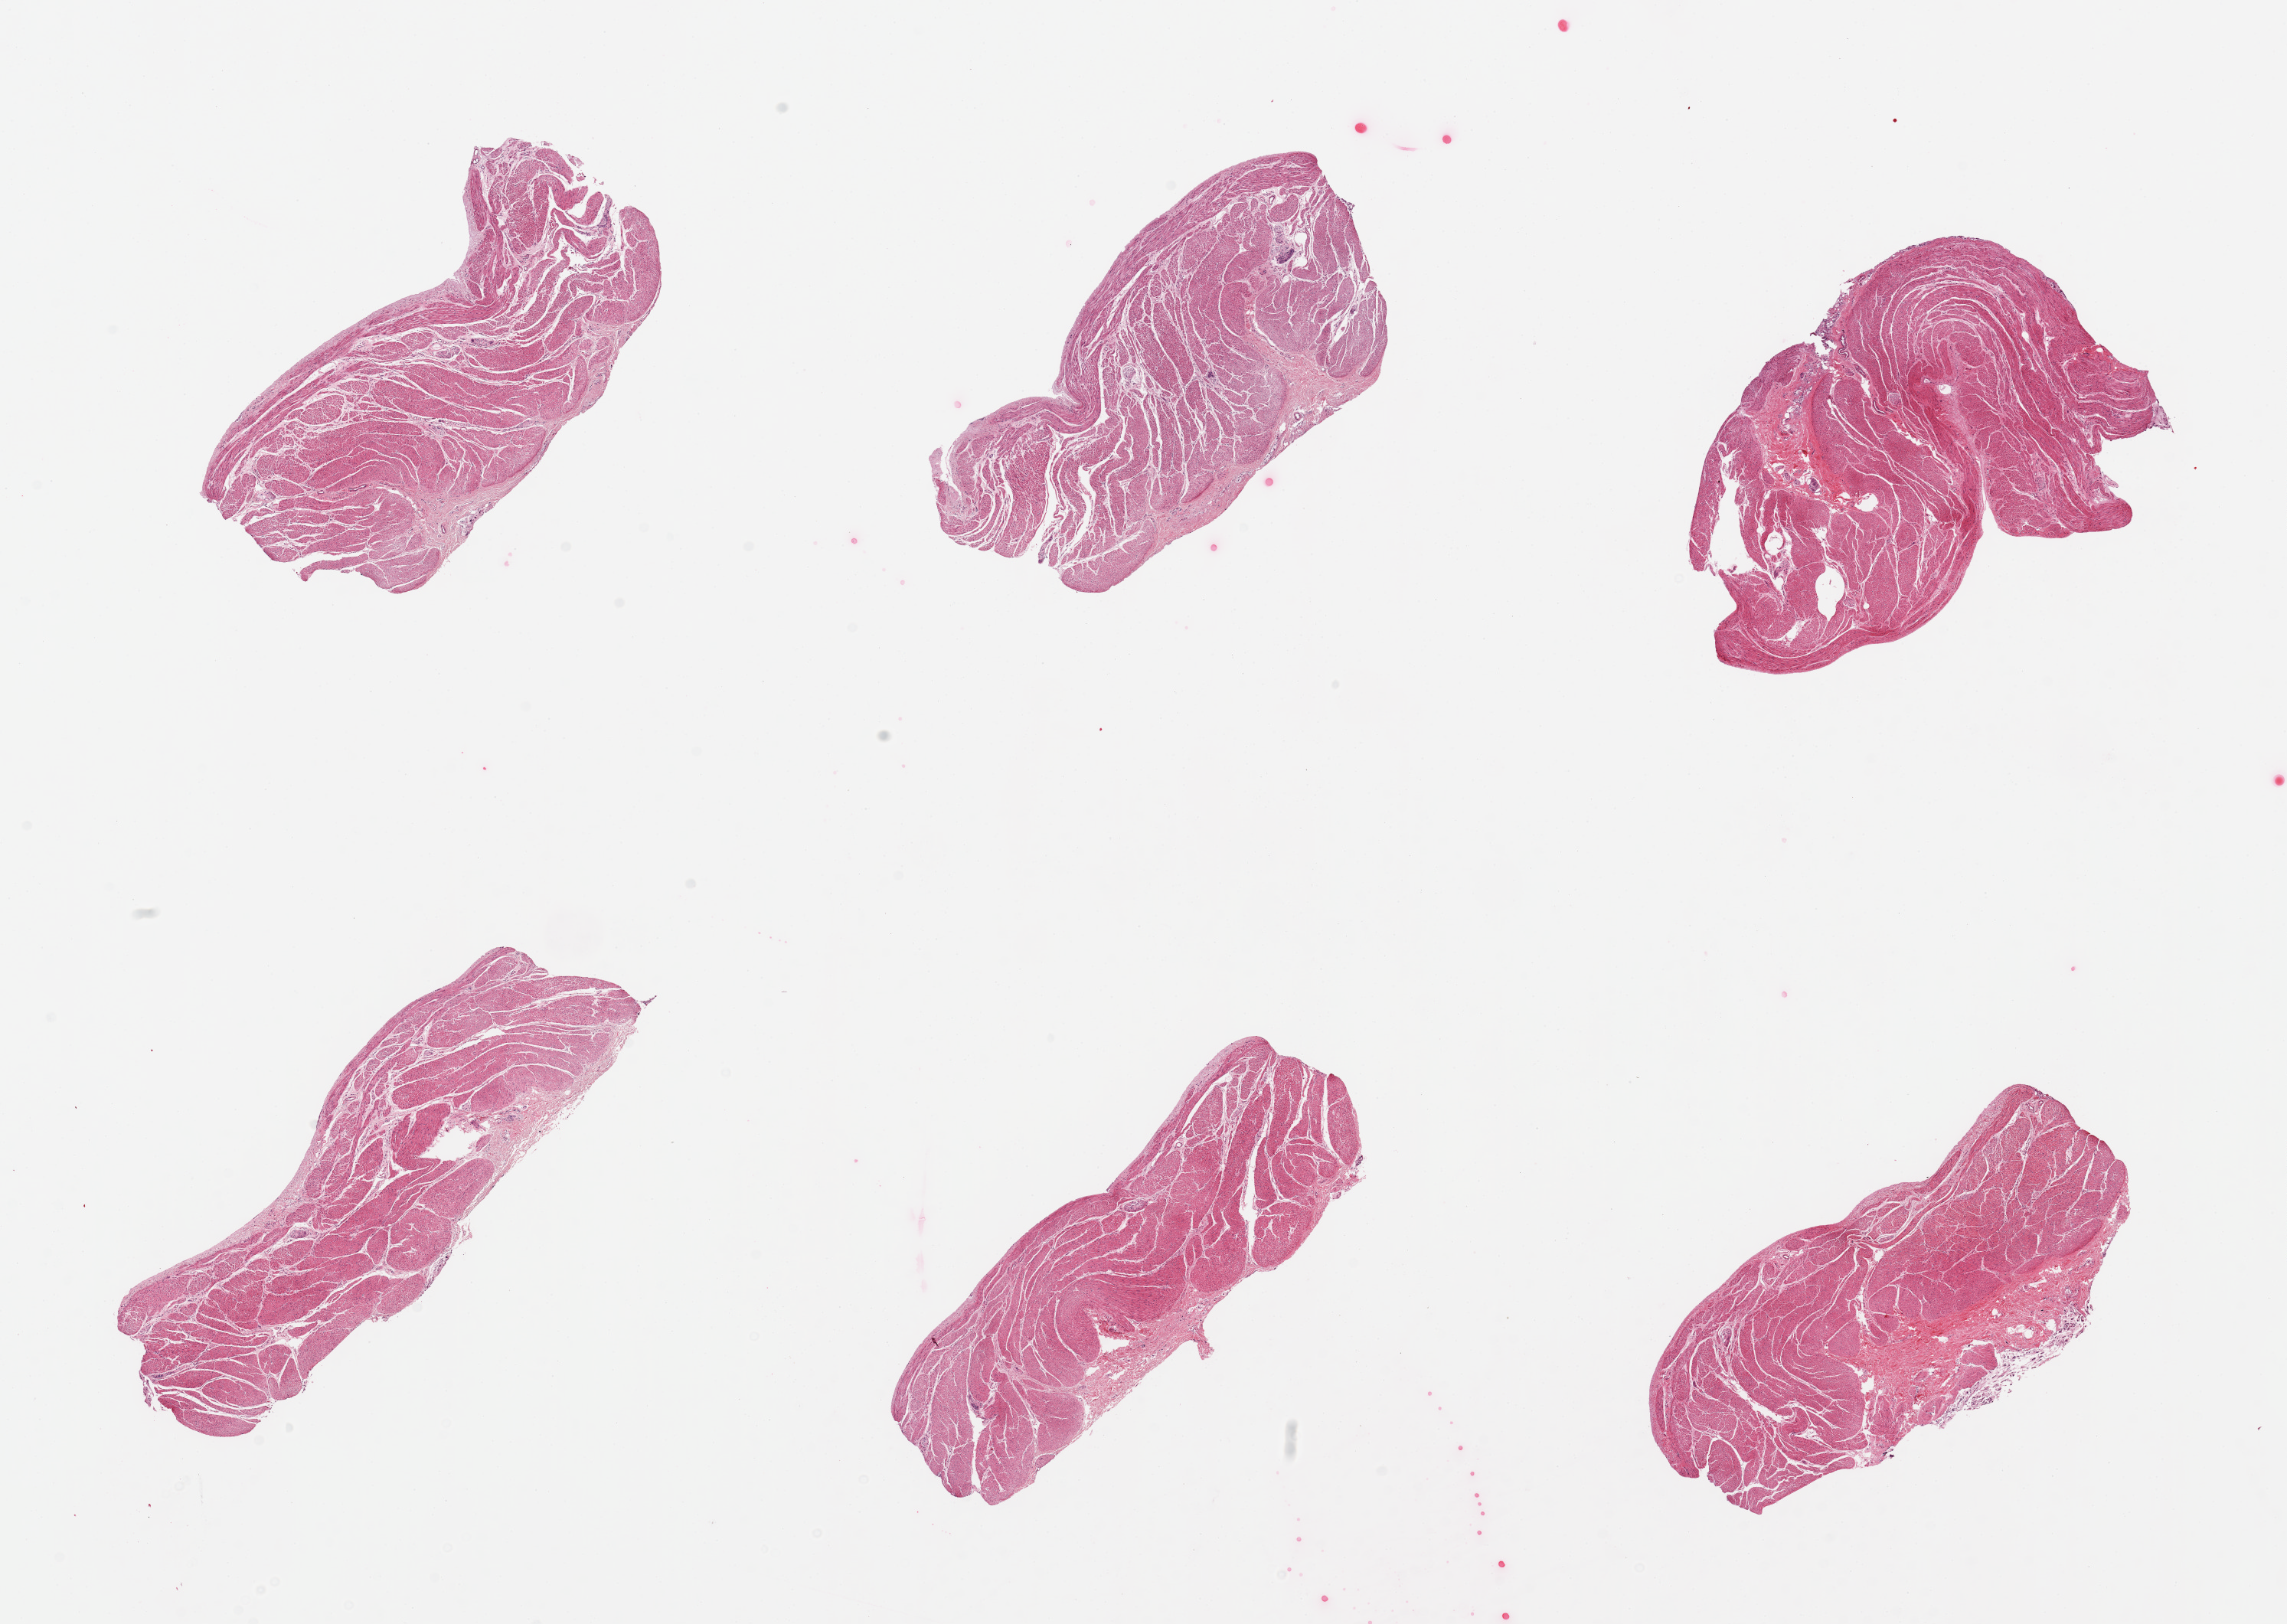
Whole-slide image, hematoxylin and eosin (H&E) stain, a low-resolution overview of the entire scanned area, about 23.6 x 16.8 mm; PAXgene-fixed paraffin-embedded (PFPE) section; section of stomach (target tissue); donor tissue sample. Donor sex: male.
Reviewer comment on this tissue sample: 6 pieces; only muscle present, no mucosa.